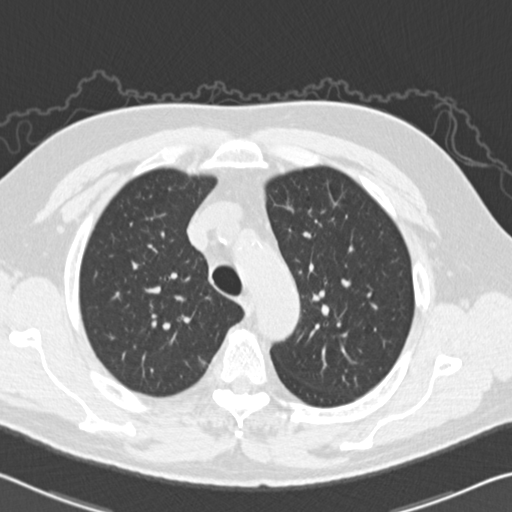
Low-dose screening chest CT, one axial slice; position 117 of 151 along the scan axis; reconstruction kernel B30f; 120 kVp; lung window (W 1500 / L -600 HU); 2 mm slice thickness; 512 × 512 image matrix, field of view 340 × 340 mm.
Structures marked on this image (expert manual segmentation):
- lesion 1 (tumor, upper lobe of right lung): bounding box <202,361,205,364> (left, top, right, bottom; pixels)